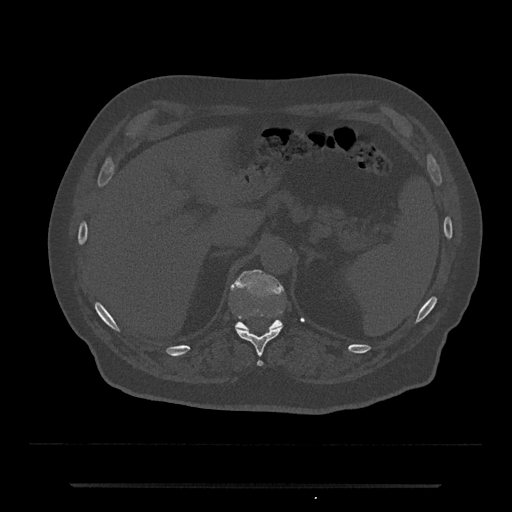
CT including the spine, one axial slice. Position 630 of 797 along the scan axis. Reconstruction kernel Br40s/3. Bone window (W 1800 / L 400 HU). 512 × 512 image matrix. Male patient, age 80 years. From the clinical record (not read from this slice): primary cancer: prostate.
Outlined on this slice (semi-automatically segmented with operator editing):
- T11 vertebra: box from (x=236, y=327) to (x=282, y=367) px
- T12 vertebra: (x=231, y=269)–(x=284, y=331)